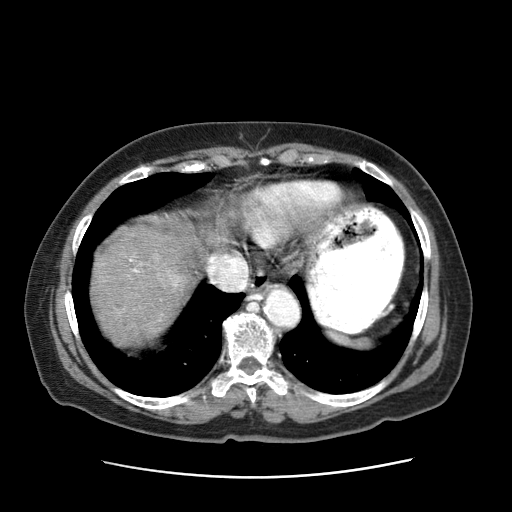
Contrast-enhanced abdominal CT (liver protocol), one axial slice. 120 kVp. Intravenous contrast given. Soft-tissue window (W 400 / L 40 HU). 512 × 512 image matrix, field of view 360 × 360 mm. Female patient, age 79 years. Case-level facts recorded for this patient, not image findings: diagnosis: hepatocellular carcinoma (patient treated with transarterial chemoembolisation; whether this scan precedes or follows treatment is not stated here); TNM stage (as recorded): Stage-II; Child-Pugh class: B; tumour differentiation: well differentiated; tumour nodularity: multinodular.
Annotated regions visible in this slice (semi-automatic segmentation, software-assisted and operator-edited):
- abdominal aorta: bounding box [x1, y1, x2, y2] px = [263, 289, 299, 326]
- liver parenchyma outside the tumour (the mass and vessels are separate outlines, so this box may not span the whole liver): [90, 214, 209, 343]
- mass: [151, 252, 185, 294]
- liver vessels: [125, 254, 249, 315]